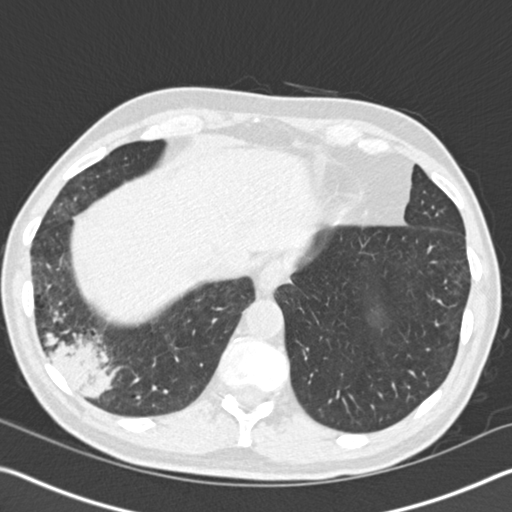
Low-dose screening chest CT, axial slice, baseline annual screen, lung window (W 1500 / L -600 HU). Male, age 61 years at enrolment.
Lesion marked by an expert reader, box from (x=11, y=275) to (x=137, y=414) px. Reader record for this screening exam (exam-level; its link to the box is not recorded): non-calcified nodule or mass ≥4 mm, right lower lobe, 52 × 36 mm, spiculated (stellate) margins, soft tissue attenuation. Participant outcome: lung cancer diagnosed 392 days after this screen — bronchiolo-alveolar adenocarcinoma, NOS, right lower lobe, moderately differentiated (G2), stage IIIB (AJCC 6th edition), 90 mm at pathology.